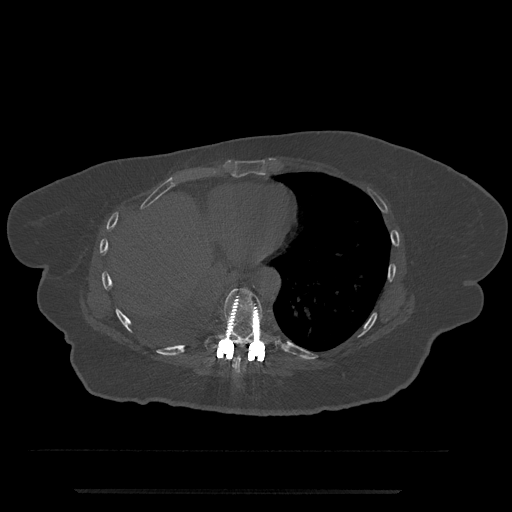
CT including the spine, one axial slice. Slice 347 of 797 in the series (ordered by position). Reconstruction kernel Br40s/3. Bone window (W 1800 / L 400 HU). 0.5 mm slice thickness. 512 × 512 image matrix, field of view 440 × 440 mm. Patient: female, 51 years. From the clinical record (not read from this slice): primary cancer: neuro; vertebrae with lytic lesions (as recorded): T8.
Annotated regions visible in this slice (semi-automatically segmented with operator editing):
- T8 vertebra: bounding box (x1, y1, x2, y2) in pixels: (233, 345, 250, 374)
- T9 vertebra: (204, 288, 277, 362)